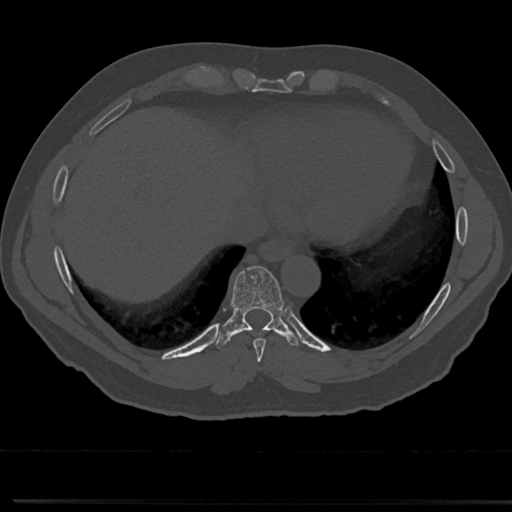
CT including the spine, one axial slice; position 319 of 817 along the scan axis; reconstruction kernel Br40s/3; 120 kVp; bone window (W 1800 / L 400 HU); 0.5 mm slice thickness; 512 × 512 image matrix, field of view 355 × 355 mm. Patient: male, 61 years. From the clinical record (not read from this slice): primary cancer: prostate.
Outlined on this slice (semi-automatically segmented with operator editing):
- T7 vertebra: bounding box (x1, y1, x2, y2) in pixels: (258, 363, 266, 376)
- T8 vertebra: (218, 267, 305, 356)